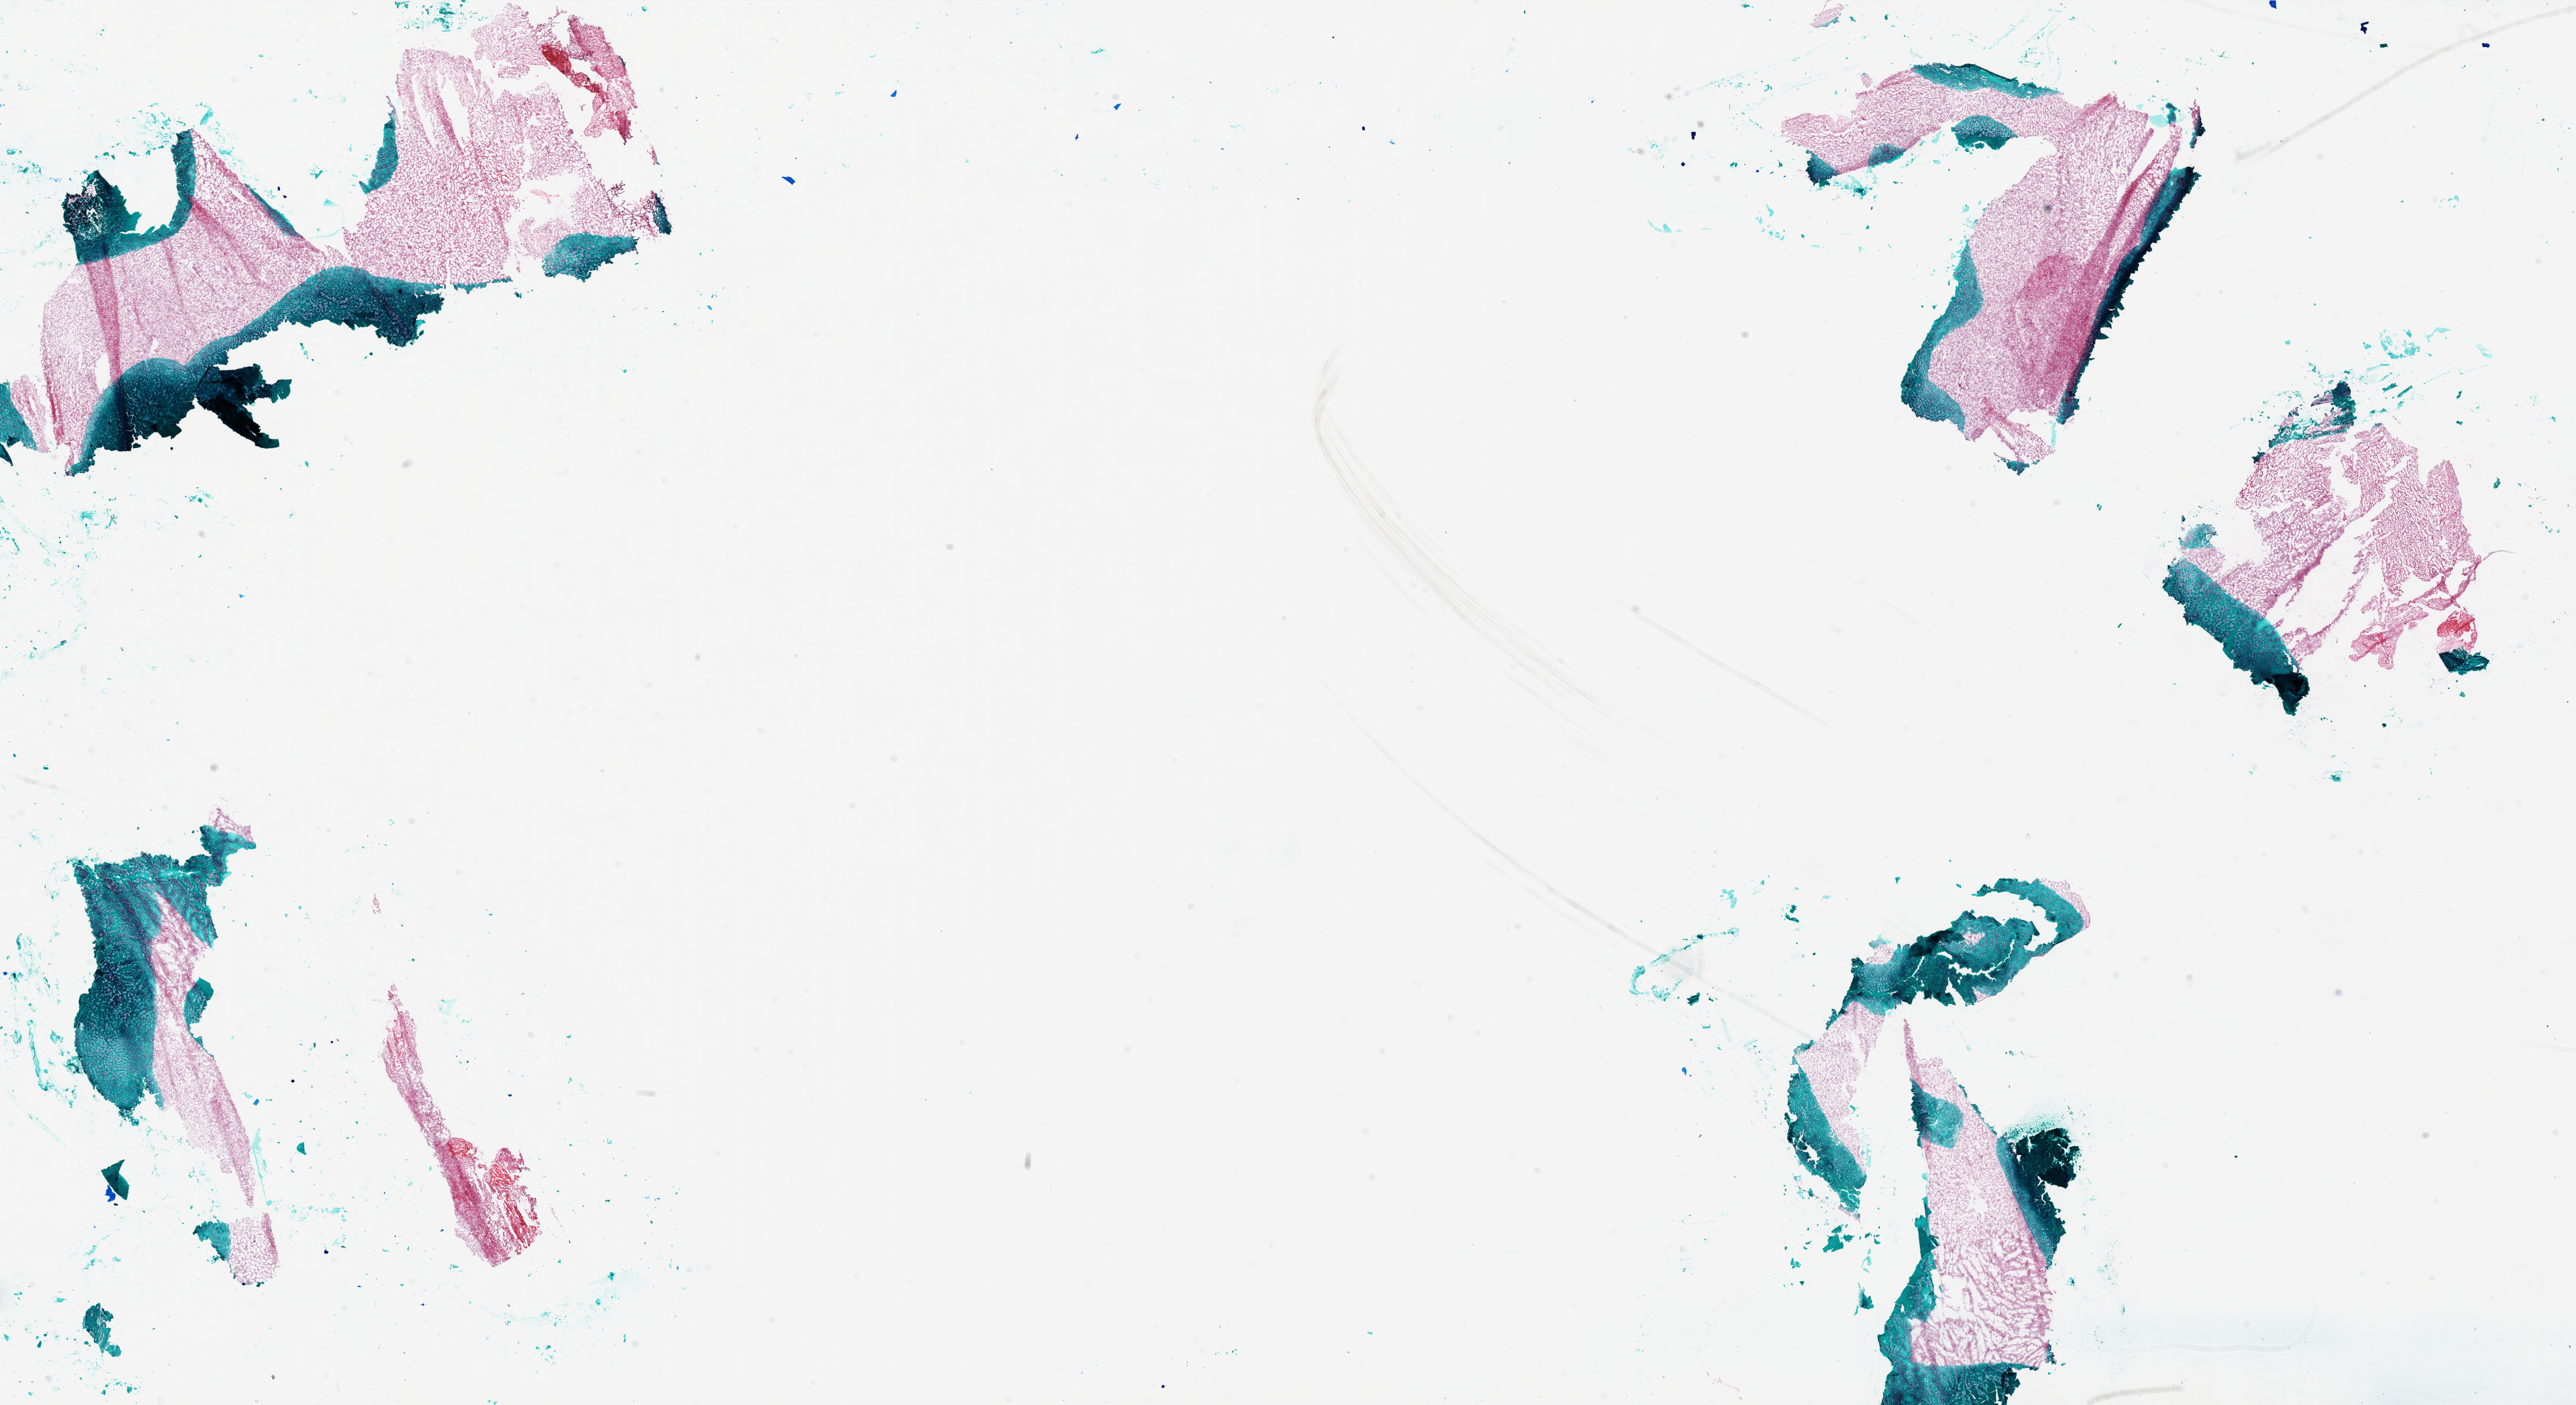
Digitized H&E-stained tissue section (whole slide), shown as a low-resolution overview of the whole scanned area (about 35.0 x 19.1 mm, slide scanned at 20x), frozen section from the bottom of the tissue portion, sample: primary tumour, brain. Female patient; age at initial diagnosis 56 years. Pathologist review of this section (percent, as recorded): tumour cells 90%, tumour nuclei 100%, normal cells 0%, stromal cells 0%, necrosis 10%.
Diagnosis: Glioblastoma.